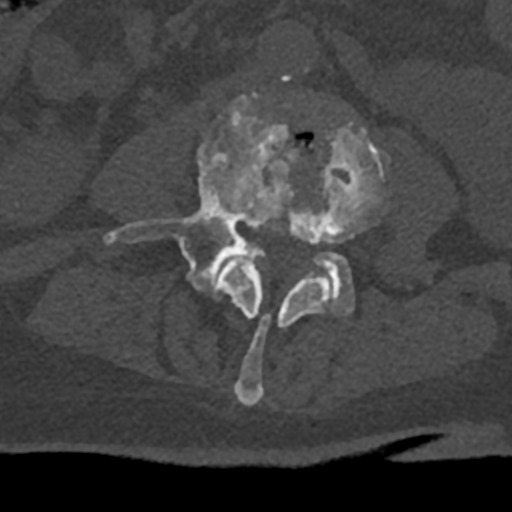
CT including the spine, one axial slice; slice 287 of 797 in the series (ordered by position); bone window (W 1800 / L 400 HU); 512 × 512 image matrix, field of view 160 × 160 mm. Patient: male, 74 years. From the clinical record (not read from this slice): primary cancer: renal.
Outlined on this slice (semi-automatically segmented with operator editing):
- L3 vertebra: bounding box (x1, y1, x2, y2) in pixels: (217, 120, 390, 406)
- L4 vertebra: (103, 97, 354, 315)